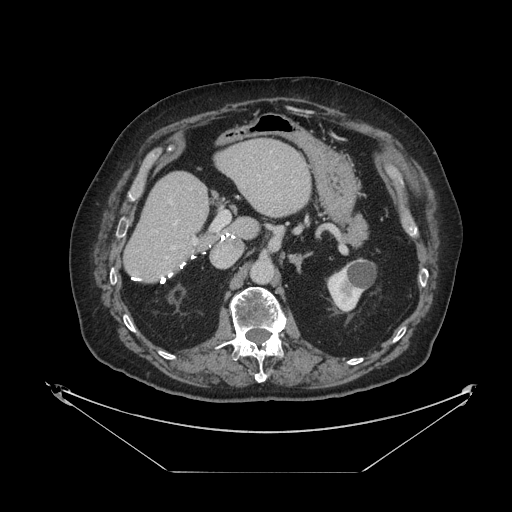
Contrast-enhanced abdominal CT, one axial slice. Slice 54 of 121 in the series (ordered by position). Reconstruction kernel STANDARD. 120 kVp. Soft-tissue window (W 400 / L 40 HU). 2.5 mm slice thickness. 512 × 512 image matrix, field of view 500 × 500 mm. Male patient, age 68 years. Case-level facts recorded for this patient, not image findings: diagnosis: colorectal cancer liver metastases, imaged before liver resection; multiple liver metastases: no; largest metastasis: 4 cm; chemotherapy before resection: yes.
Annotated regions visible in this slice (expert manual segmentation):
- hepatic veins: box from (x=175, y=167) to (x=277, y=225) px
- liver: (x=125, y=140)–(x=311, y=282)
- planned liver remnant (the part of the liver to remain after resection): (x=125, y=140)–(x=311, y=282)
- portal vein (with intrahepatic branches): (x=170, y=201)–(x=230, y=249)